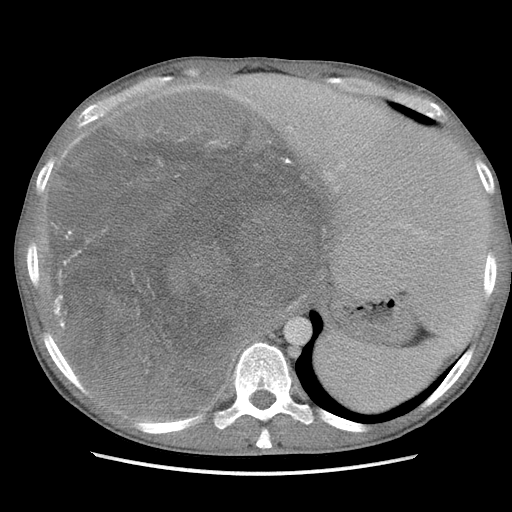
Contrast-enhanced abdominal CT, one axial slice. Position 83 of 115 along the scan axis. Soft-tissue window (W 400 / L 40 HU). 5 mm slice thickness. 512 × 512 image matrix, field of view 360 × 360 mm. Male patient. Case-level facts recorded for this patient, not image findings: diagnosis: adrenocortical carcinoma; tumour side: right adrenal; Ki-67 index: 13 %; stage (as recorded): 3.
Structures marked on this image (semi-automatically segmented with operator editing):
- mass: box from (x=53, y=88) to (x=317, y=417) px